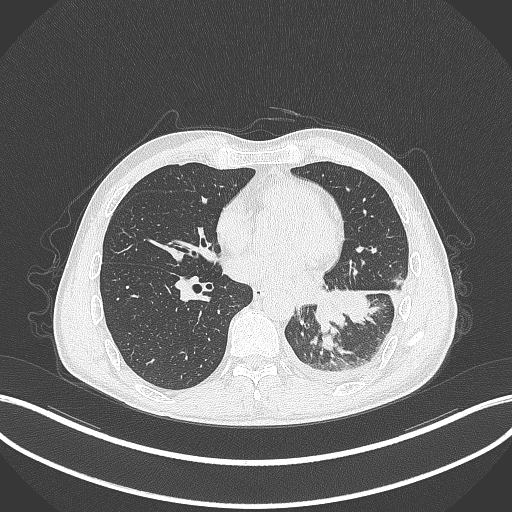
Chest CT, one axial slice. Slice 131 of 295 in the series (ordered by position). Lung window (W 1500 / L -600 HU). 1 mm slice thickness. 512 × 512 image matrix, field of view 400 × 400 mm. Patient: male, 47 years. From the clinical record (not read from this slice): clinical TNM (as recorded): T3 N1 M1c; histopathological grade: G3.
Annotated regions visible in this slice (rectangle marked by the reading radiologist):
- lung tumour (recorded histology: small cell carcinoma): bounding box (x1, y1, x2, y2) in pixels: (310, 285, 347, 336)